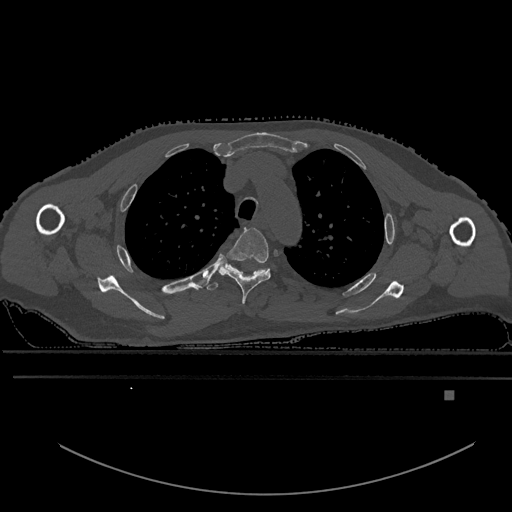
CT including the spine, one axial slice. Slice 441 of 969 in the series (ordered by position). Bone window (W 1800 / L 400 HU). 512 × 512 image matrix, field of view 456 × 456 mm. Male patient, age 82 years. From the clinical record (not read from this slice): primary cancer: prostate.
Annotated regions visible in this slice (semi-automatically segmented with operator editing):
- T3 vertebra: bounding box <218,227,271,305> (left, top, right, bottom; pixels)
- T4 vertebra: <206,261,269,291>